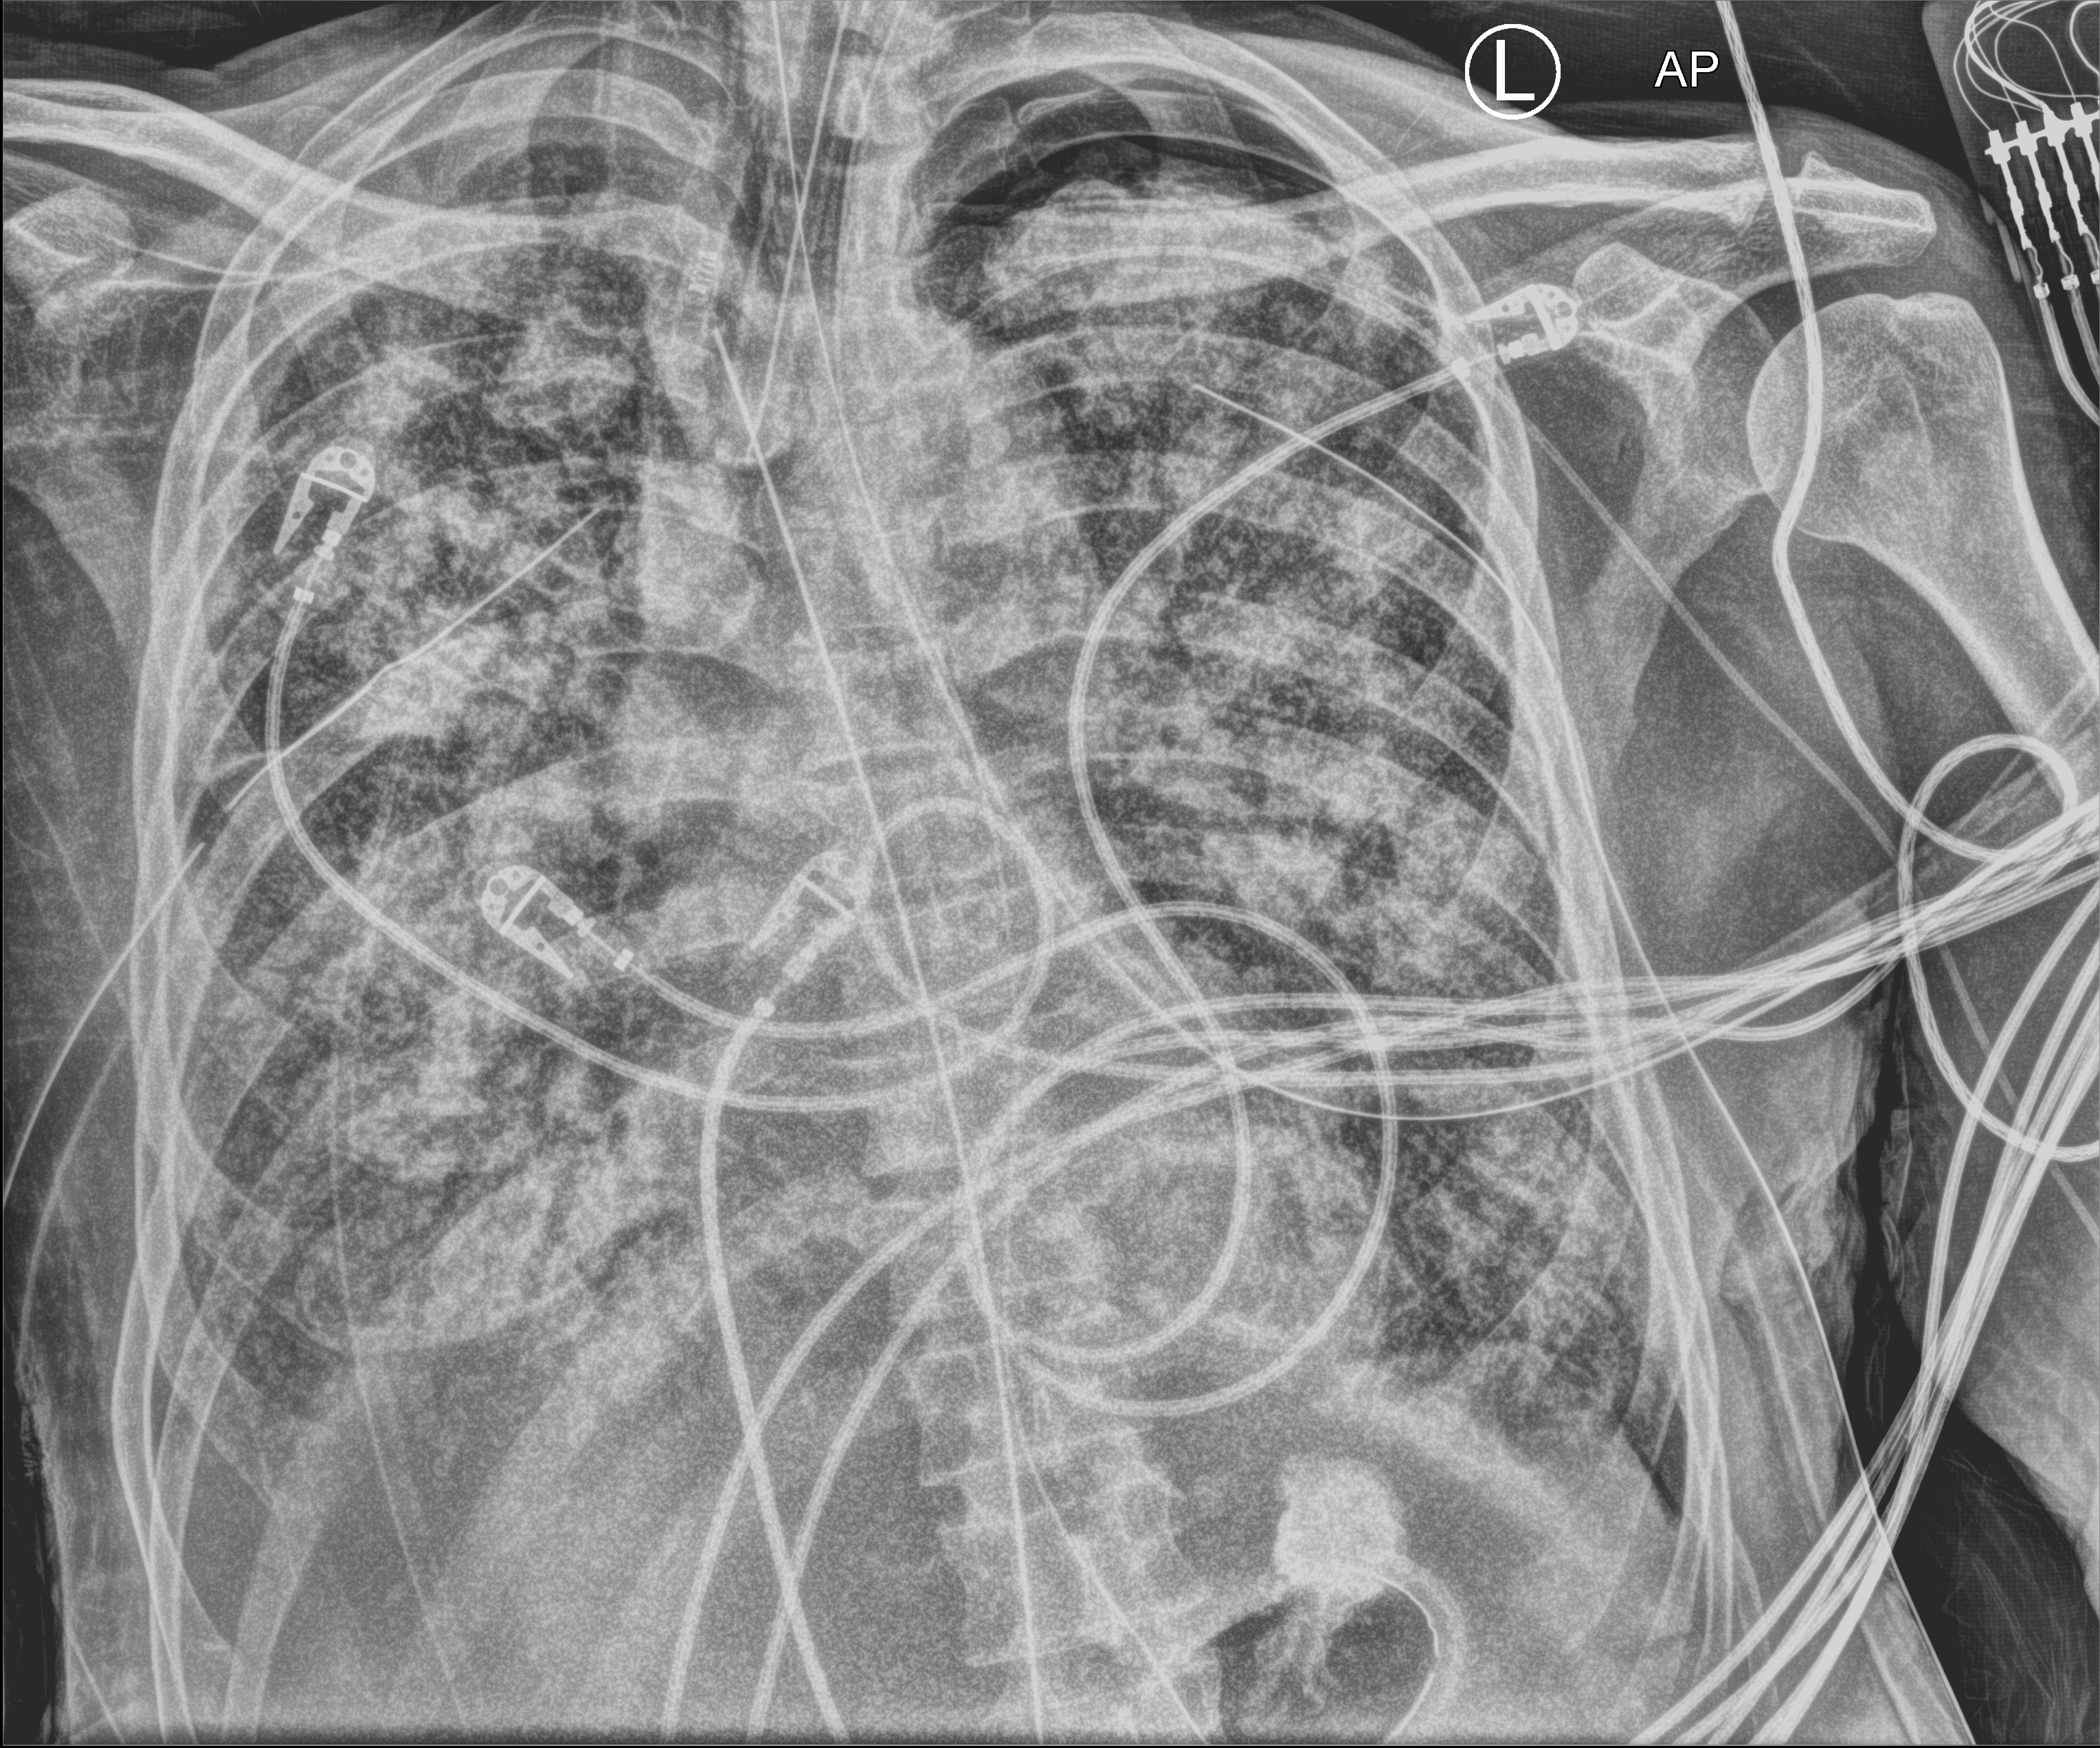
Portable chest radiograph, anteroposterior (AP) projection. Male patient hospitalised with COVID-19, age 60–74 years.
From the hospital-stay record, not from the radiograph (when in the stay this image was taken is not recorded): admitted to intensive care during this hospital stay: yes.